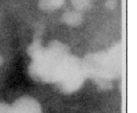
Region of interest cut from a scanned film mammogram (one marked finding), right breast, CC view.
- Finding: calcifications, morphology pleomorphic / fine linear branching, distribution segmental; BI-RADS assessment category 5; subtlety rating 5 on a 1 (subtle) to 5 (obvious) scale; pathology result (as recorded, not read from the image): malignant.